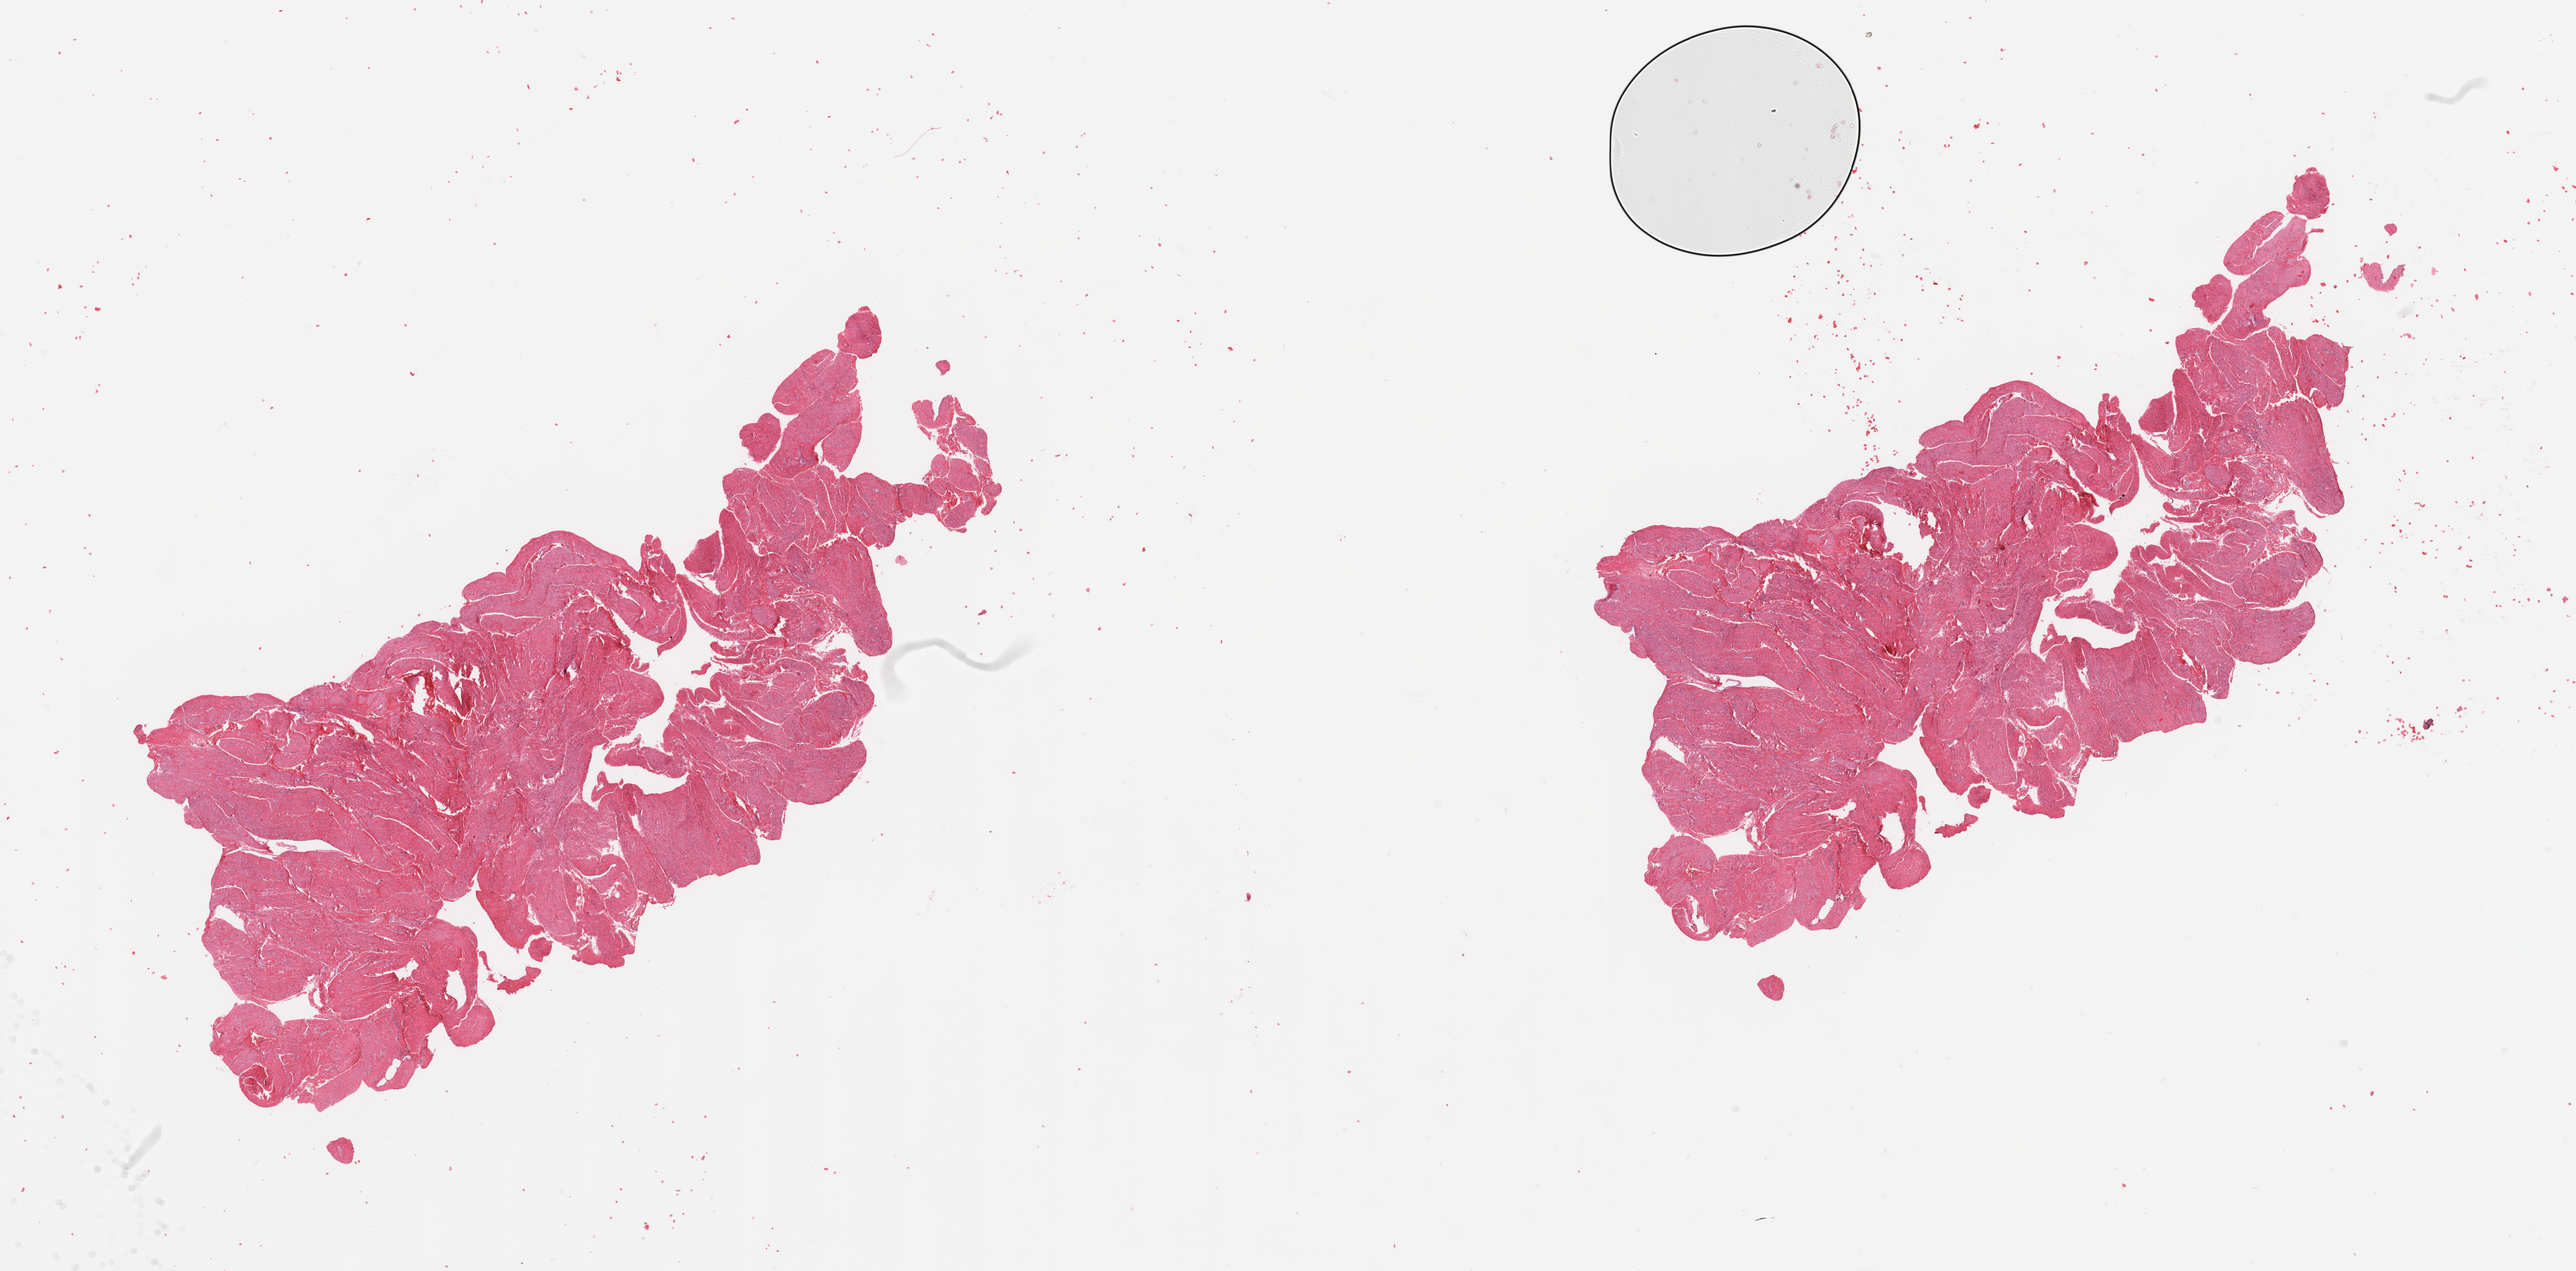
Whole-slide histology image, H&E — whole scanned area (about 31.5 x 15.5 mm, from a 20x scan) shown as a low-resolution overview; normal (non-tumour) tissue sample, uterus. Patient: female, age 53 years.
This section: normal (non-tumour) tissue from the same patient. Patient diagnosis: Endometrioid adenocarcinoma, NOS.